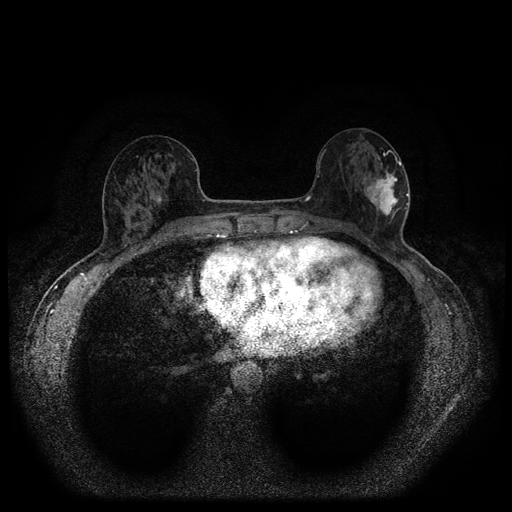
Breast MRI (dynamic contrast-enhanced, multi-phase), one axial slice. Position 44 of 116 along the scan axis. Dynamic contrast-enhanced series, time point 2 of 5 at this slice position (early post-contrast). 1.5 T. TE 2.7 ms, TR 5.4 ms. 2 mm slice thickness. 512 × 512 image matrix, field of view 330 × 330 mm. Female patient, age 56 years.
Outlined on this slice (semi-automatic segmentation, software-assisted and operator-edited):
- breast lesion (labelled 'tumour' in the annotation; benign lesions carry a separate 'benign' label): bounding box <355,168,401,217> (left, top, right, bottom; pixels)